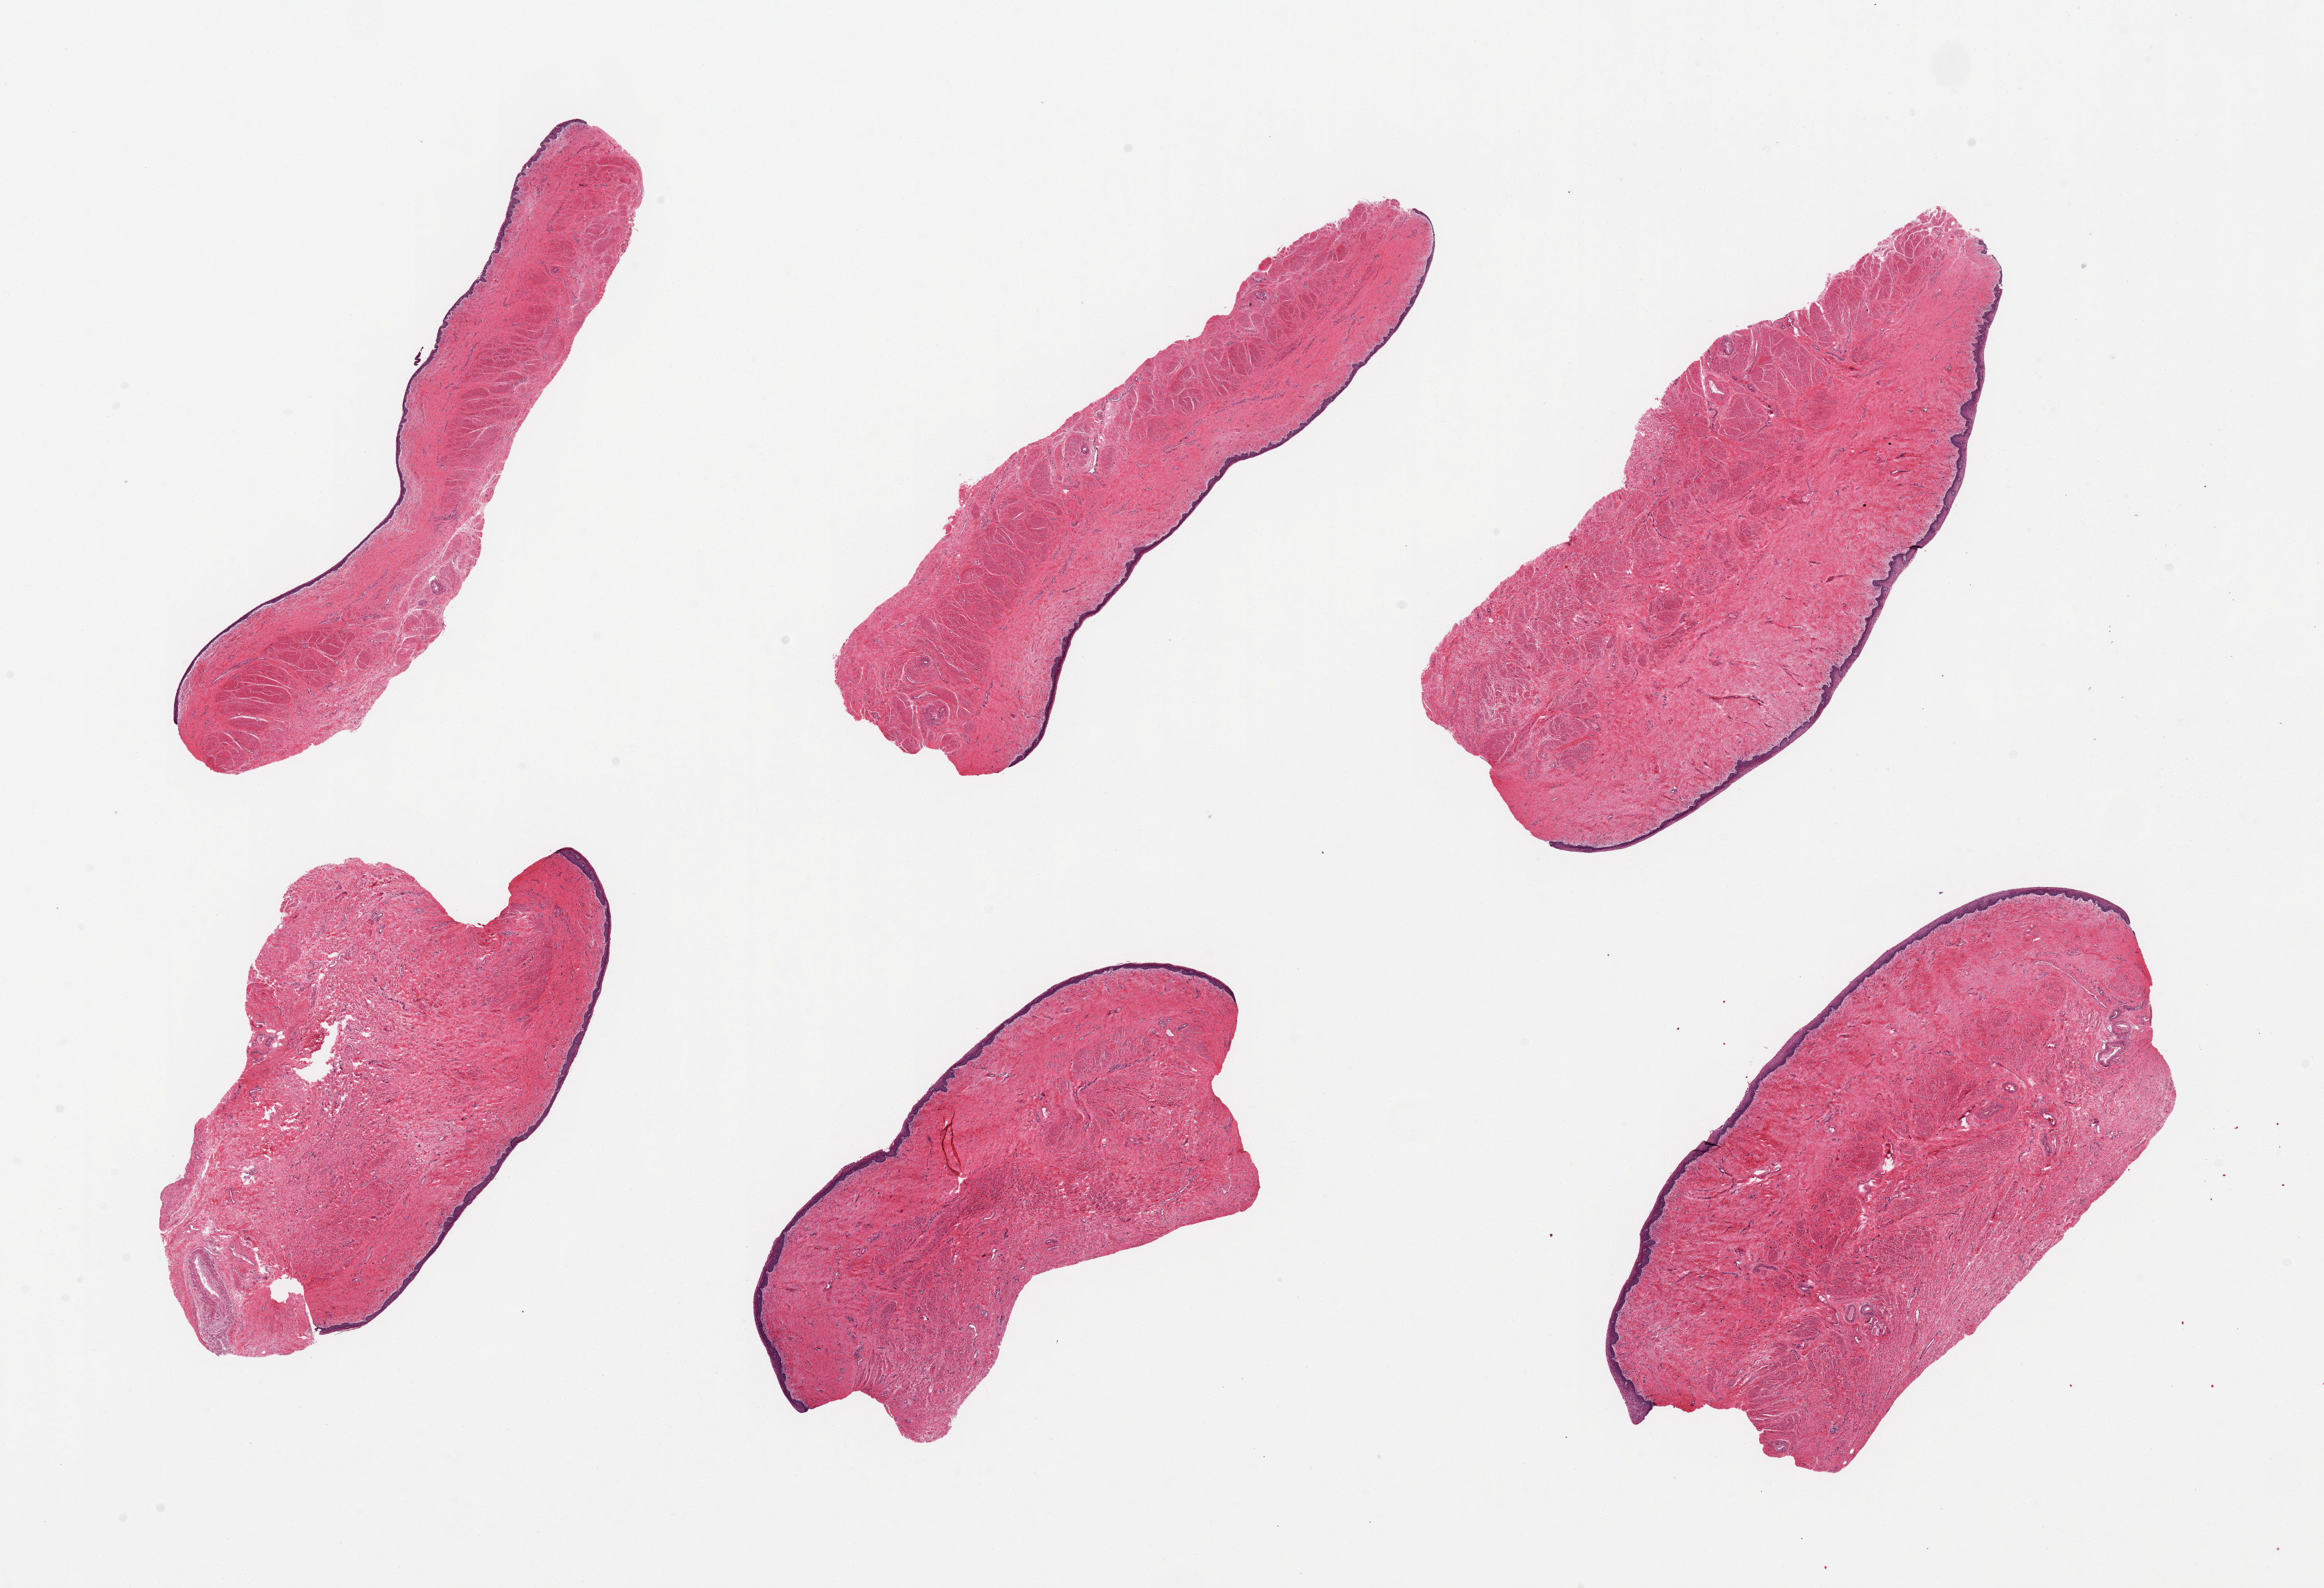
Haematoxylin and eosin whole-slide image — low-resolution overview of the scanned area, about 27.6 x 18.8 mm (acquisition: 20x scan), PAXgene-fixed, paraffin-embedded tissue, section of vagina (target tissue), donor tissue sample.
* review note (as recorded): 6 pieces; no lesions